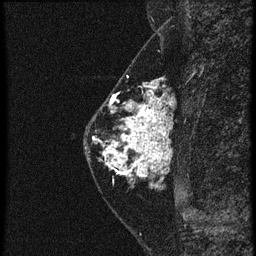
Breast MRI (dynamic contrast-enhanced), one sagittal slice. Position 23 of 60 along the scan axis. 4 images stored at this slice position (order not interpretable as contrast timing). 1.5 T. TE 4.2 ms, TR 20.4 ms. 1.5 mm slice thickness. 256 × 256 image matrix, field of view 180 × 180 mm. Female patient, age 46 years. From the clinical record (not read from this slice): setting: breast cancer imaged before/during neoadjuvant chemotherapy; receptor status: triple-negative.
Annotated regions visible in this slice (semi-automatic segmentation, software-assisted and operator-edited):
- analysis volume of interest (the breast-tissue region the enhancement analysis was run in; not a lesion): bounding box [x1, y1, x2, y2] px = [88, 82, 167, 185]
- tumour enhancement mask (voxels above the 90 % enhancement threshold inside the analysis volume of interest): [104, 86, 165, 179]